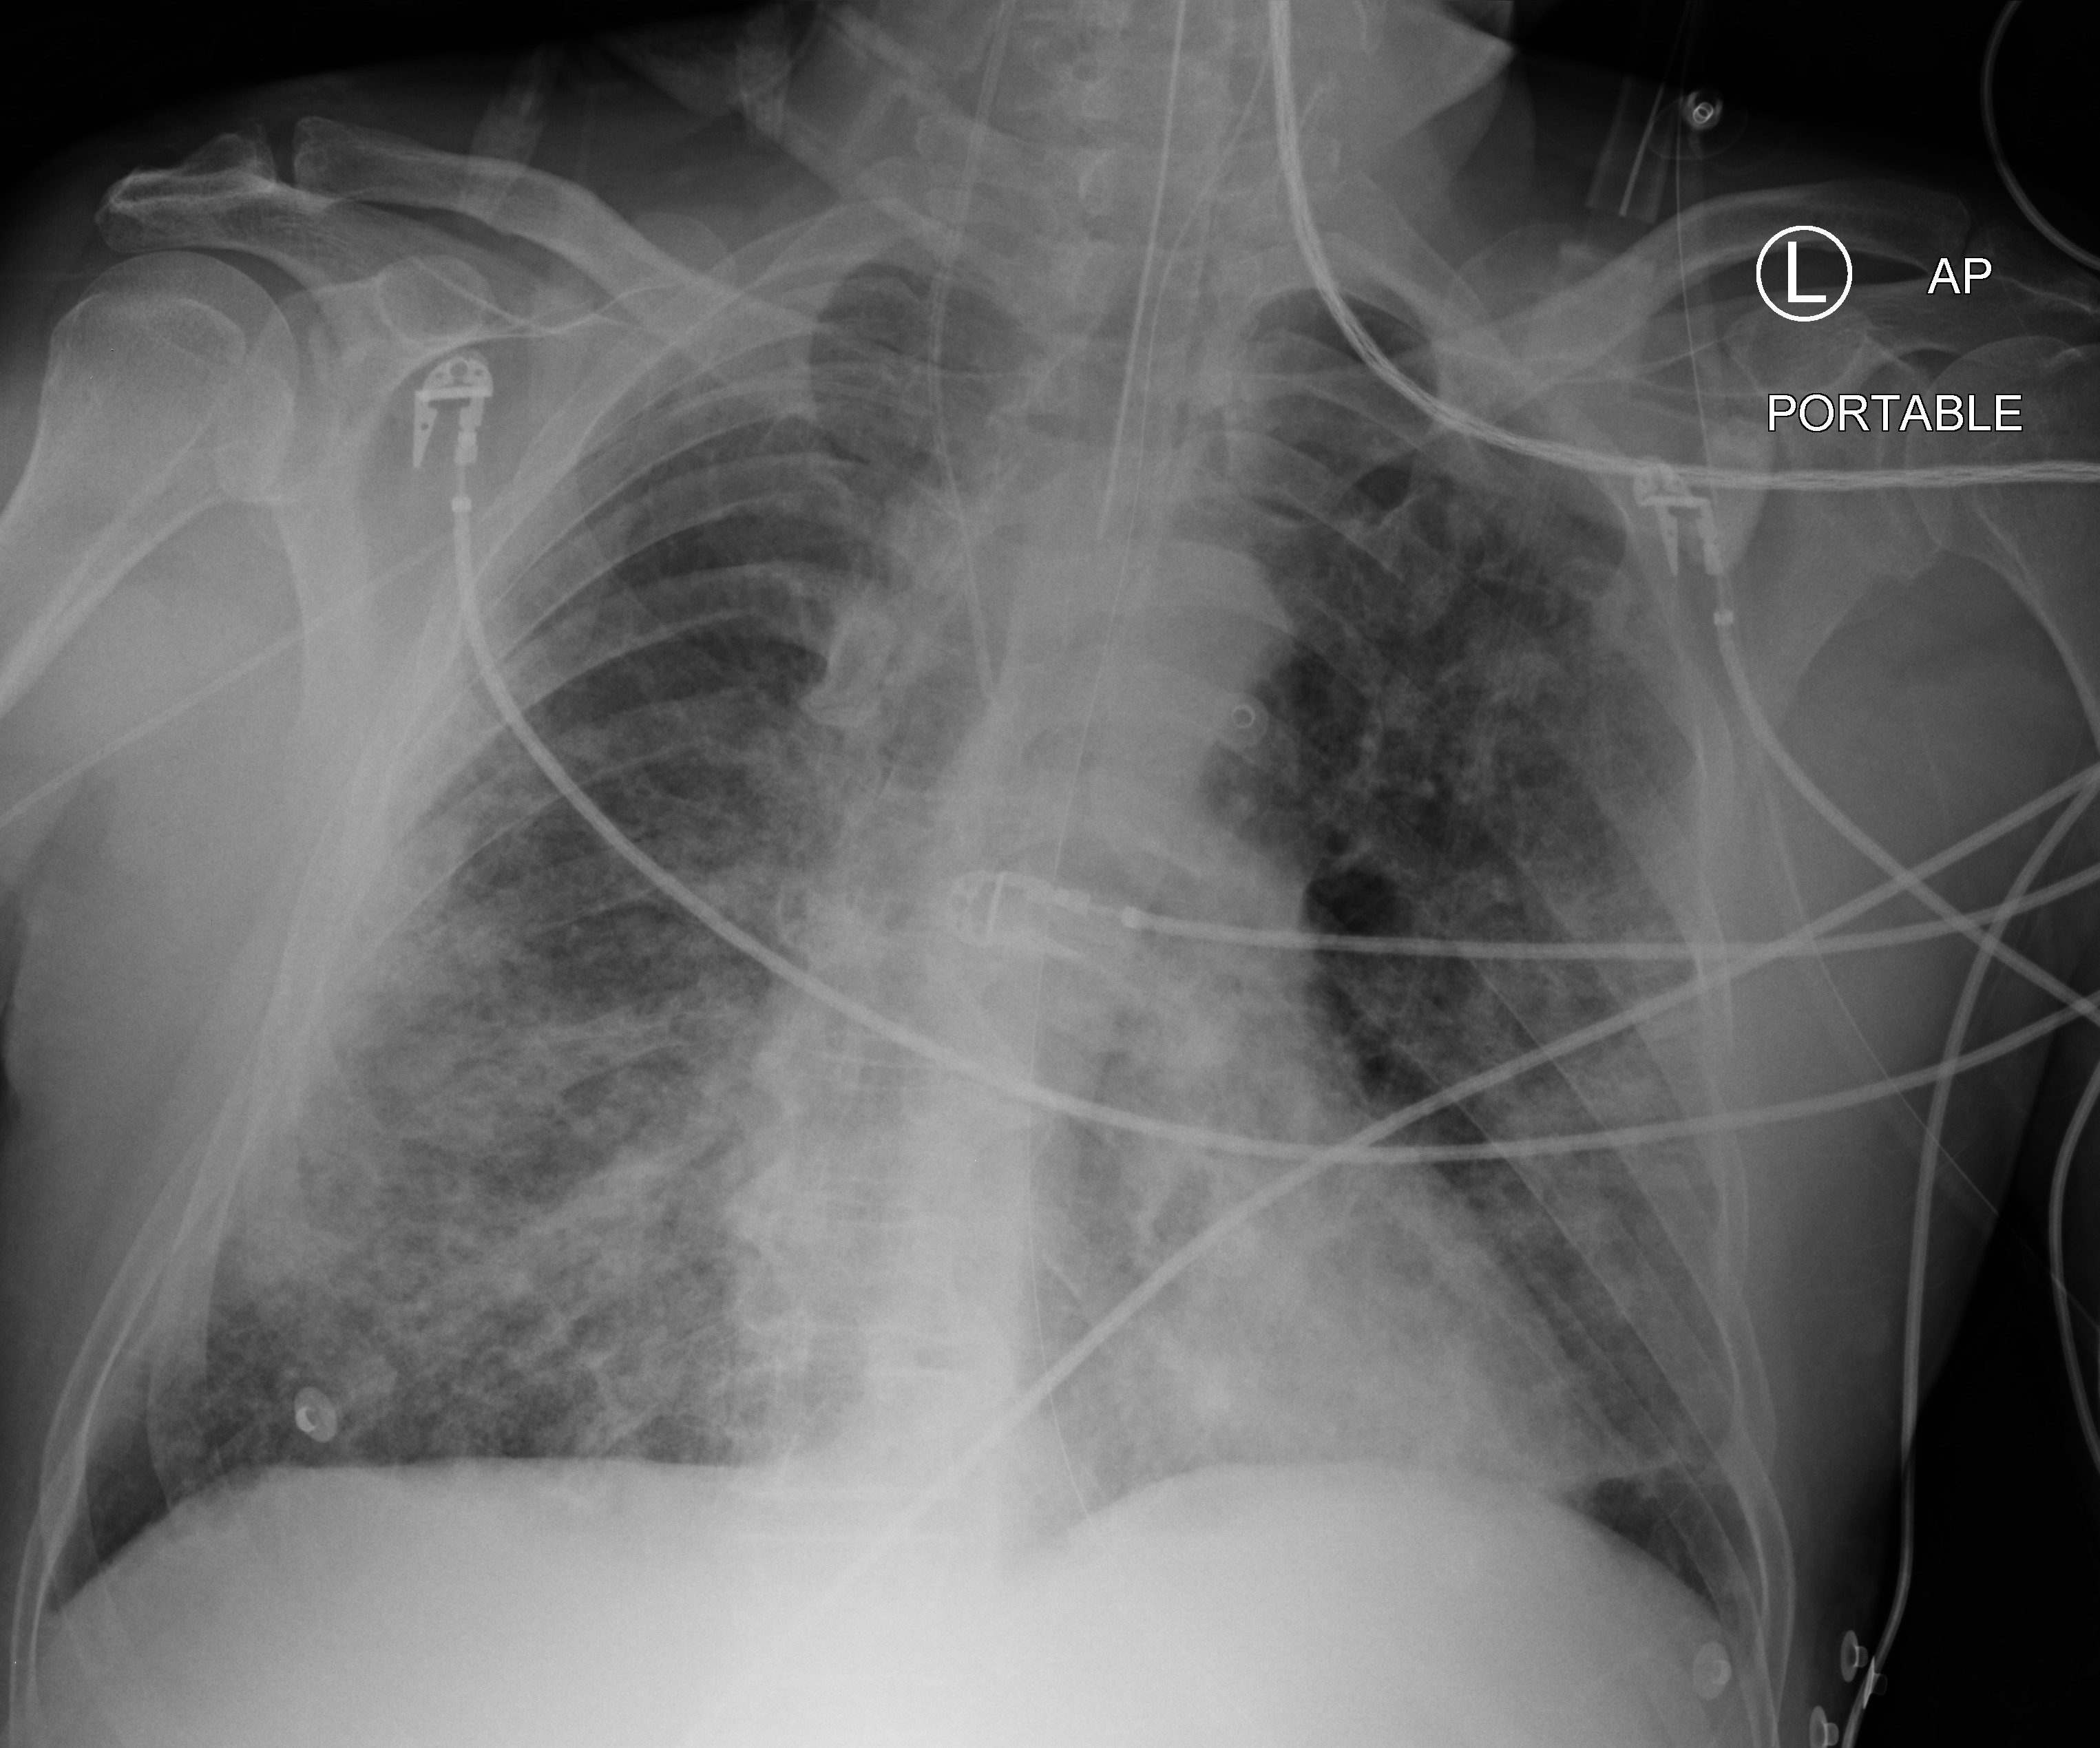
Bedside chest radiograph (computed radiography); anteroposterior (AP) projection. Male patient hospitalised with COVID-19, age 60–74 years.
Admission-level facts for this patient (not findings on this image; timing relative to this image not recorded):
- length of hospital stay: 32 days